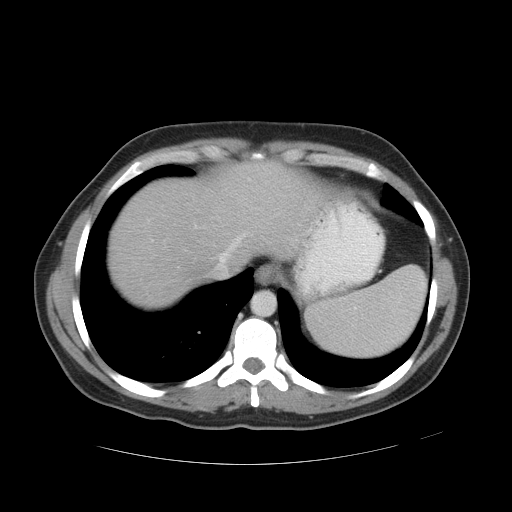
Contrast-enhanced abdominal CT, one axial slice; position 43 of 49 along the scan axis; 120 kVp; intravenous contrast given; soft-tissue window (W 400 / L 40 HU); 512 × 512 image matrix, field of view 422 × 422 mm. Male patient, age 42 years. Case-level facts recorded for this patient, not image findings: diagnosis: colorectal cancer liver metastases, imaged before liver resection; multiple liver metastases: yes; largest metastasis: 2.8 cm.
Structures marked on this image (outlined manually by an expert reader):
- hepatic veins: bounding box <151,201,280,276> (left, top, right, bottom; pixels)
- liver: <109,163,312,309>
- planned liver remnant (the part of the liver to remain after resection): <109,163,312,309>